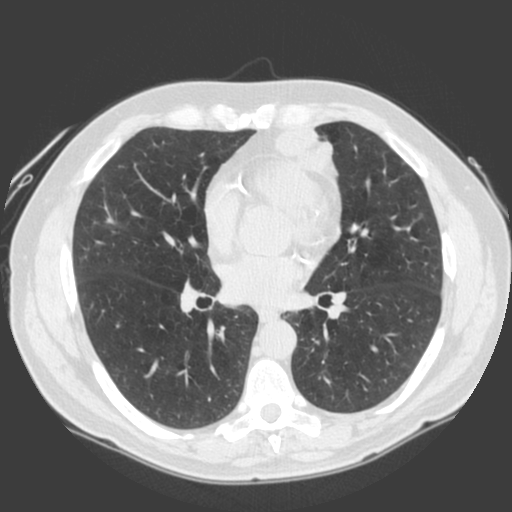
Low-dose screening chest CT, one axial slice. 120 kVp. Lung window (W 1500 / L -600 HU). 2 mm slice thickness. 512 × 512 image matrix, field of view 360 × 360 mm.
Outlined on this slice (expert manual segmentation):
- lesion 1 (tumor, lower lobe of left lung): bounding box <275,124,336,179> (left, top, right, bottom; pixels)